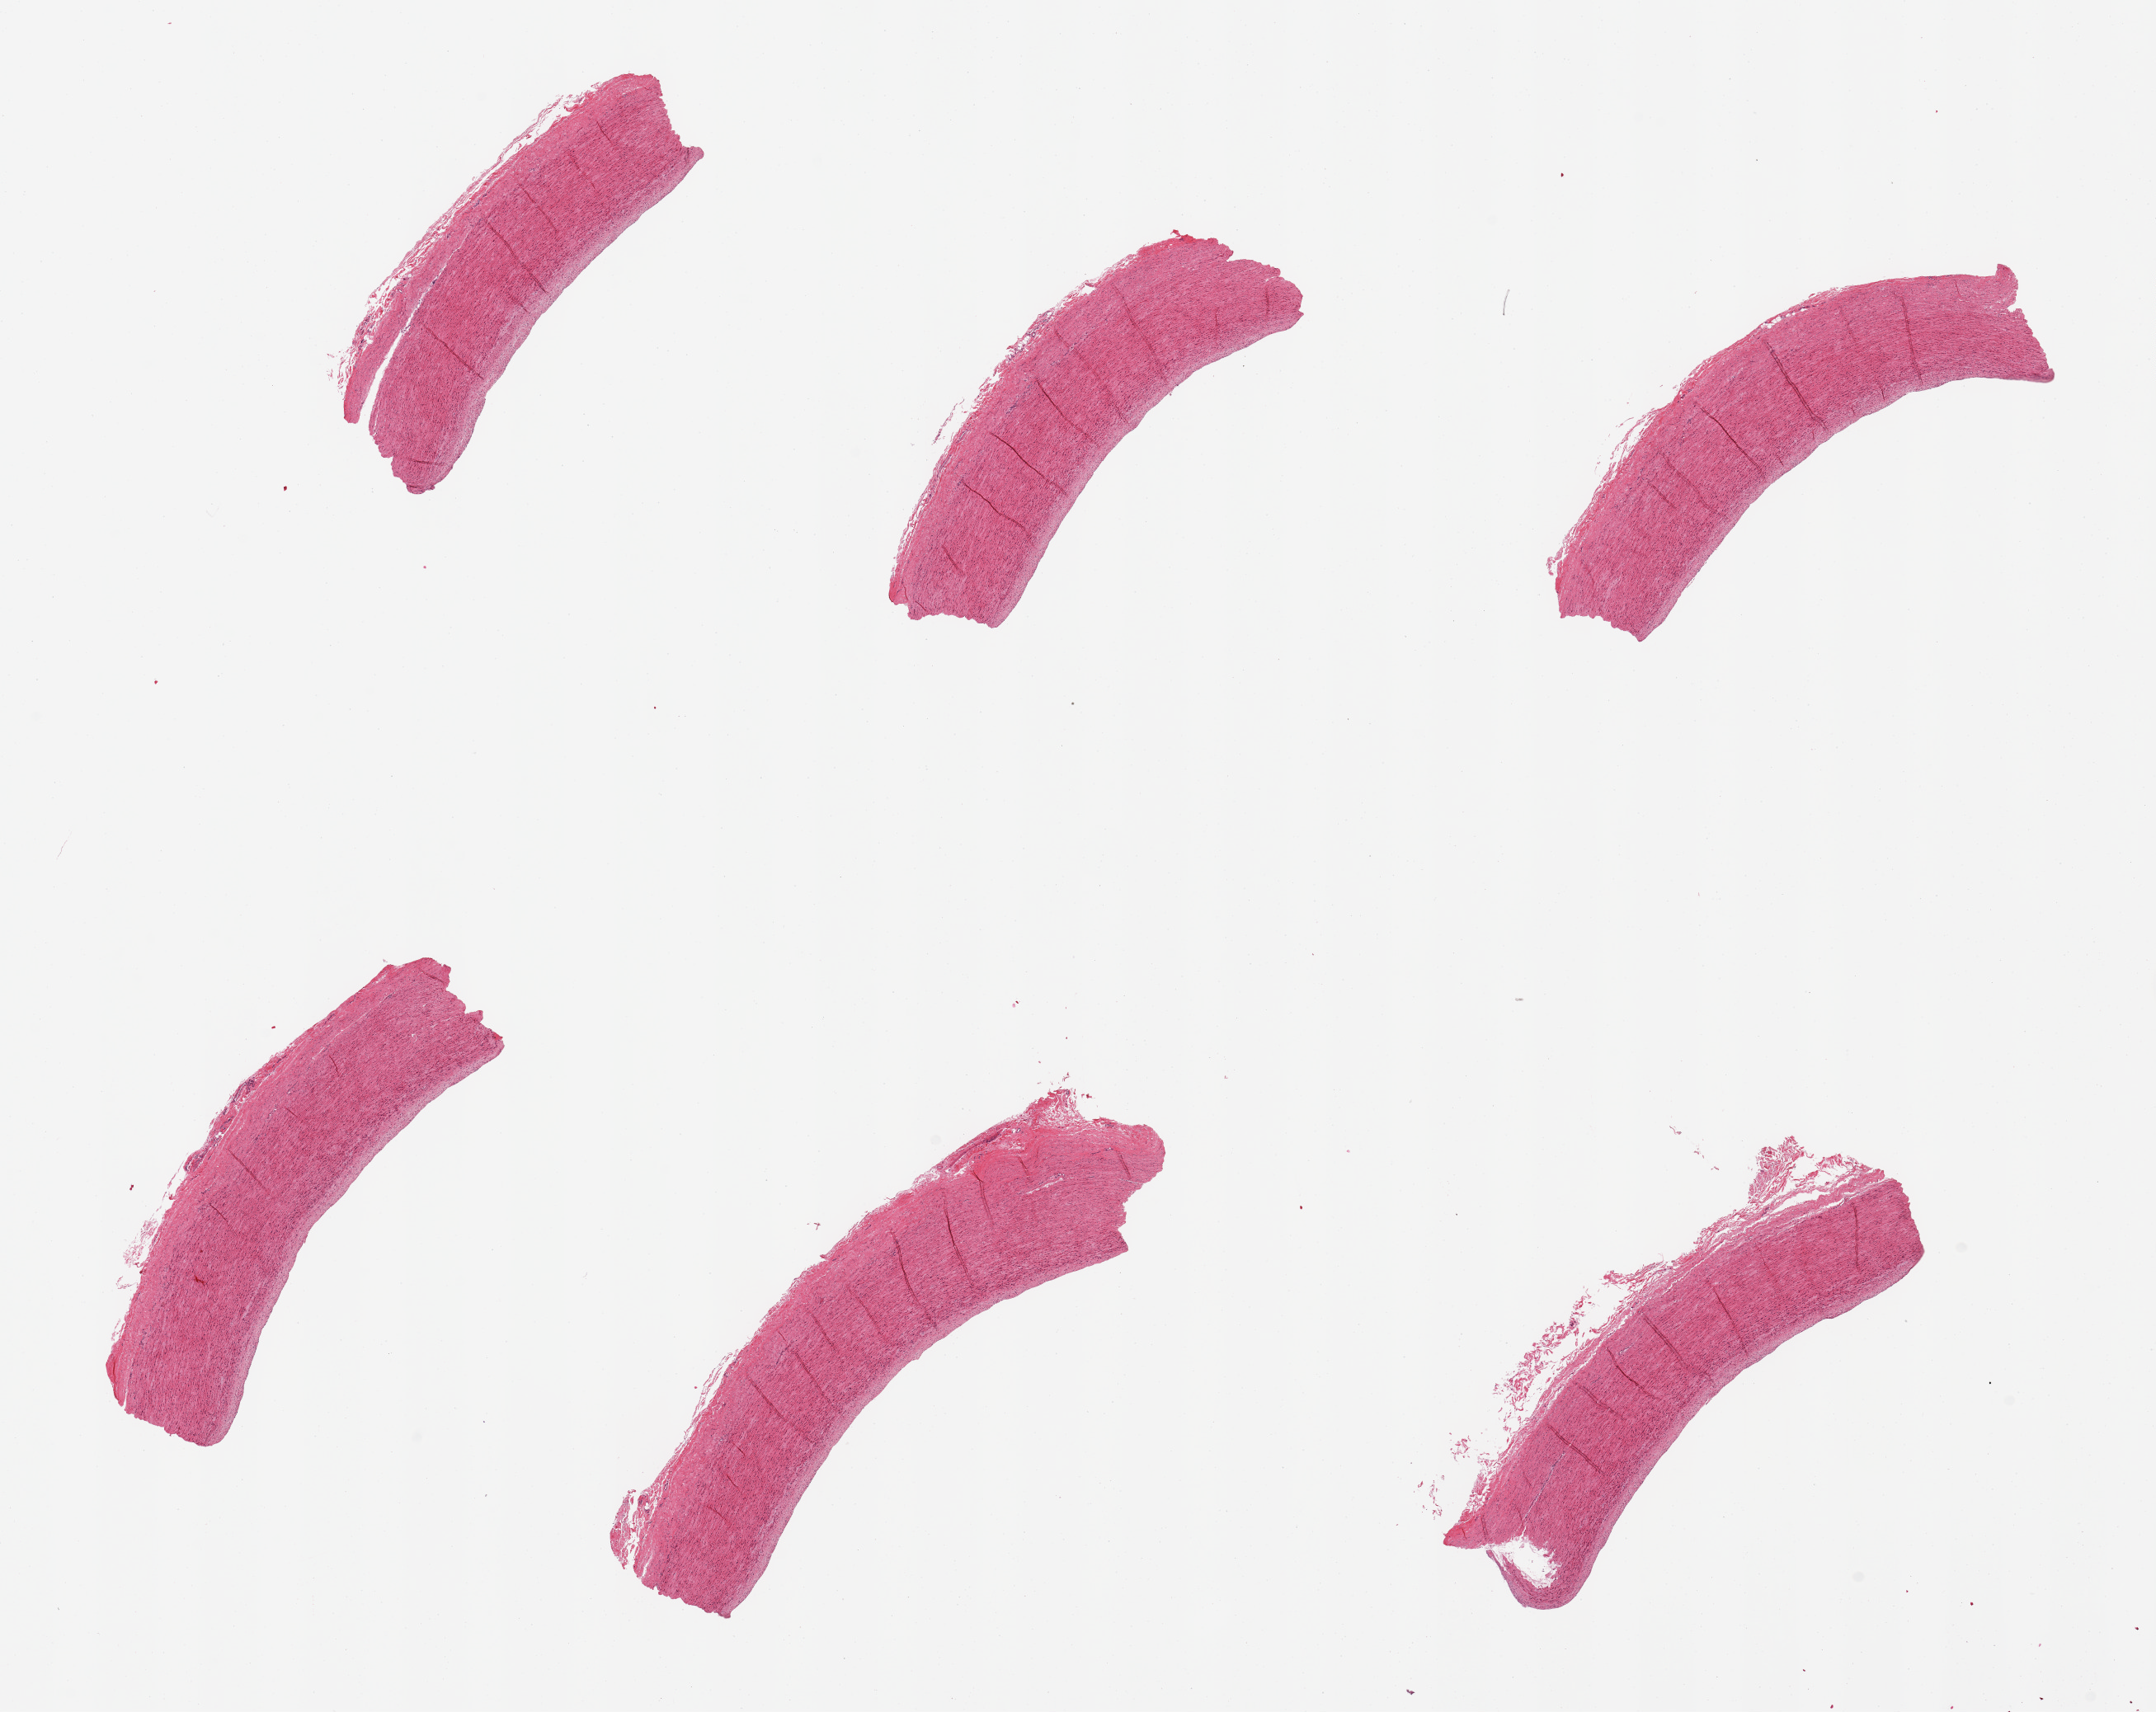
Haematoxylin and eosin whole-slide image — whole scanned area (about 20.7 x 16.4 mm) shown as a low-resolution overview; PAXgene-fixed paraffin-embedded (PFPE) section; target tissue: aorta; tissue donor sample. Male donor.
Reviewer comment on this tissue sample: 6 pieces, minimal atherosis, ~0.15mm.